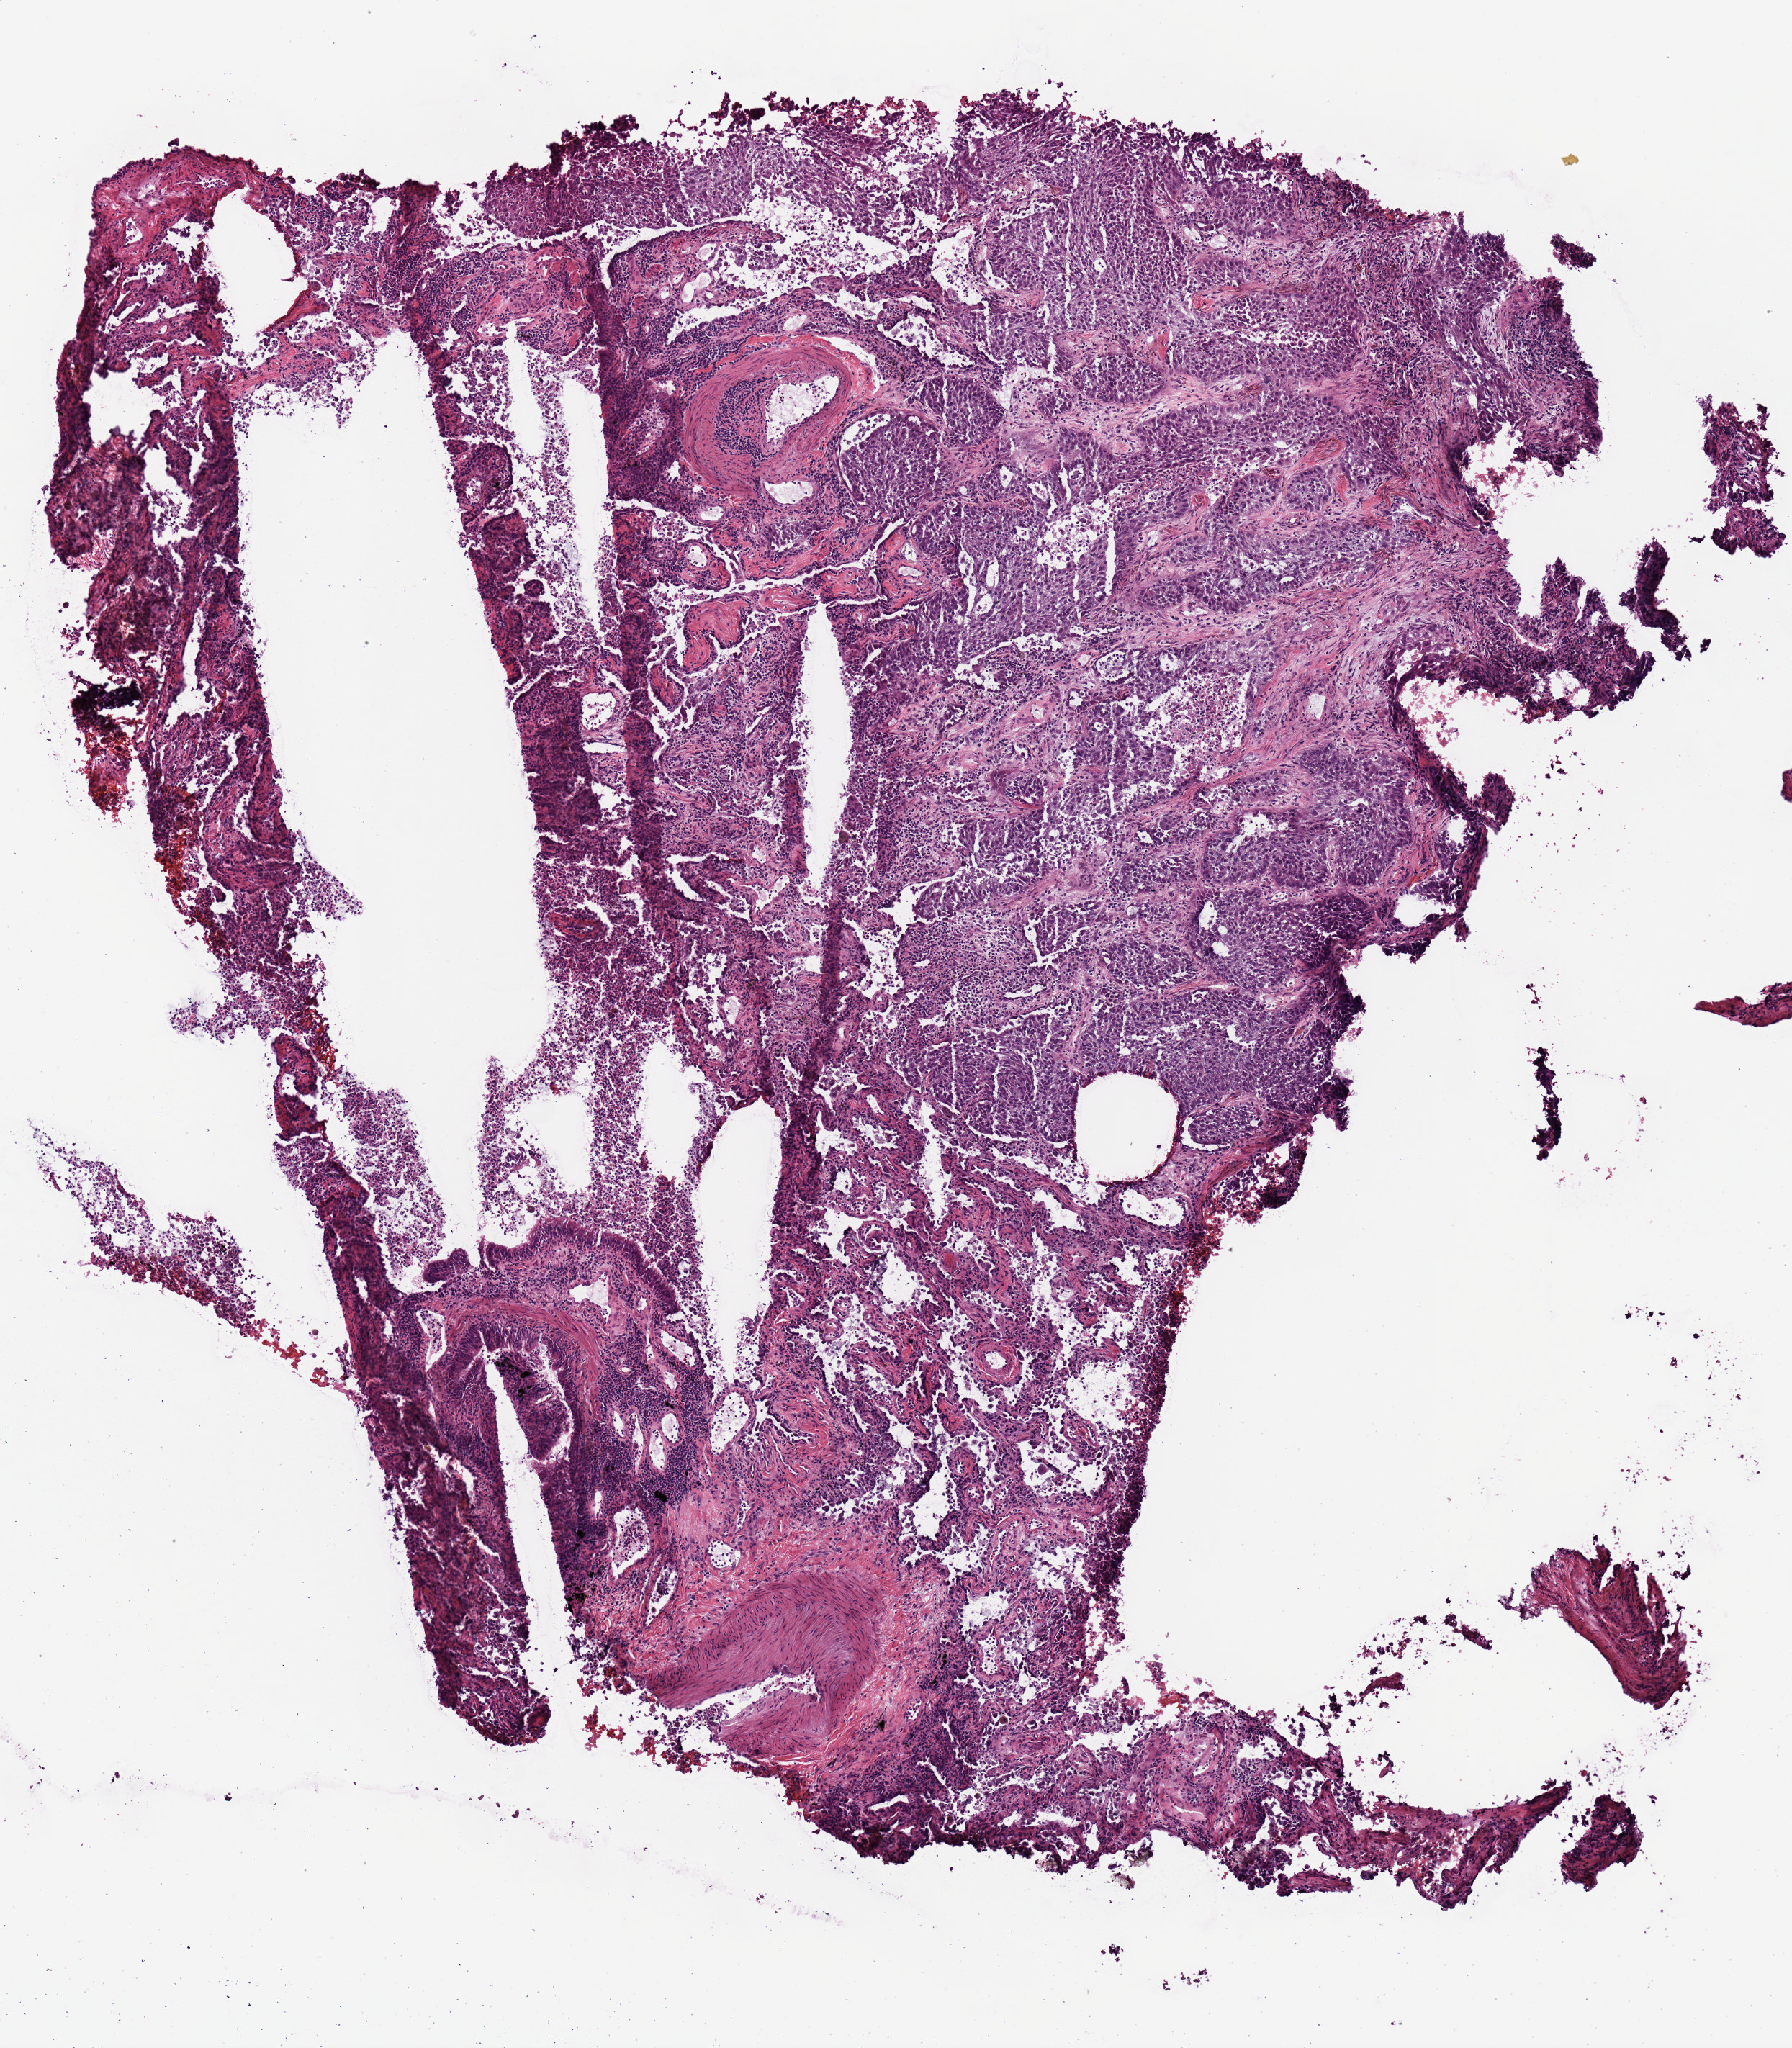
Whole-slide histology image, H&E, a low-resolution overview of the entire scanned area, about 4.9 x 5.6 mm. Frozen section from the top of the tissue portion. Lung, primary tumour sample. Male, age 72 years at initial diagnosis. Slide review estimates, as recorded: tumour cells 70%, tumour nuclei 70%, normal cells 0%, stromal cells 15%, necrosis 15%.
• AJCC pathologic stage: IA
• laterality: right
• pathologic diagnosis: Squamous cell carcinoma, NOS (upper lobe, lung)